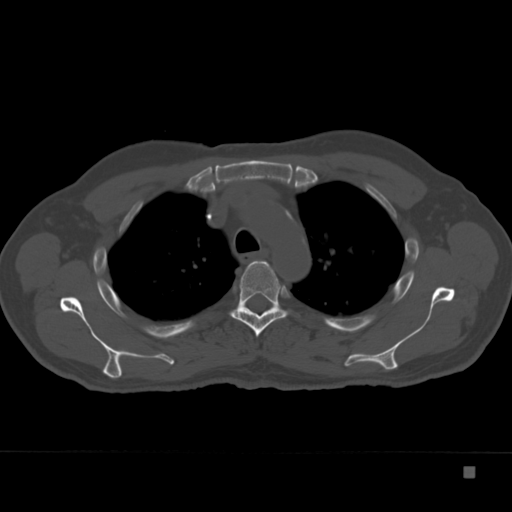
CT including the spine, one axial slice. Slice 272 of 332 in the series (ordered by position). Bone window (W 1800 / L 400 HU). 1.5 mm slice thickness. 512 × 512 image matrix, field of view 389 × 389 mm. Male patient, age 72 years. From the clinical record (not read from this slice): primary cancer: skeletal.
Structures marked on this image (semi-automatic segmentation, software-assisted and operator-edited):
- T4 vertebra: box from (x=230, y=260) to (x=287, y=337) px